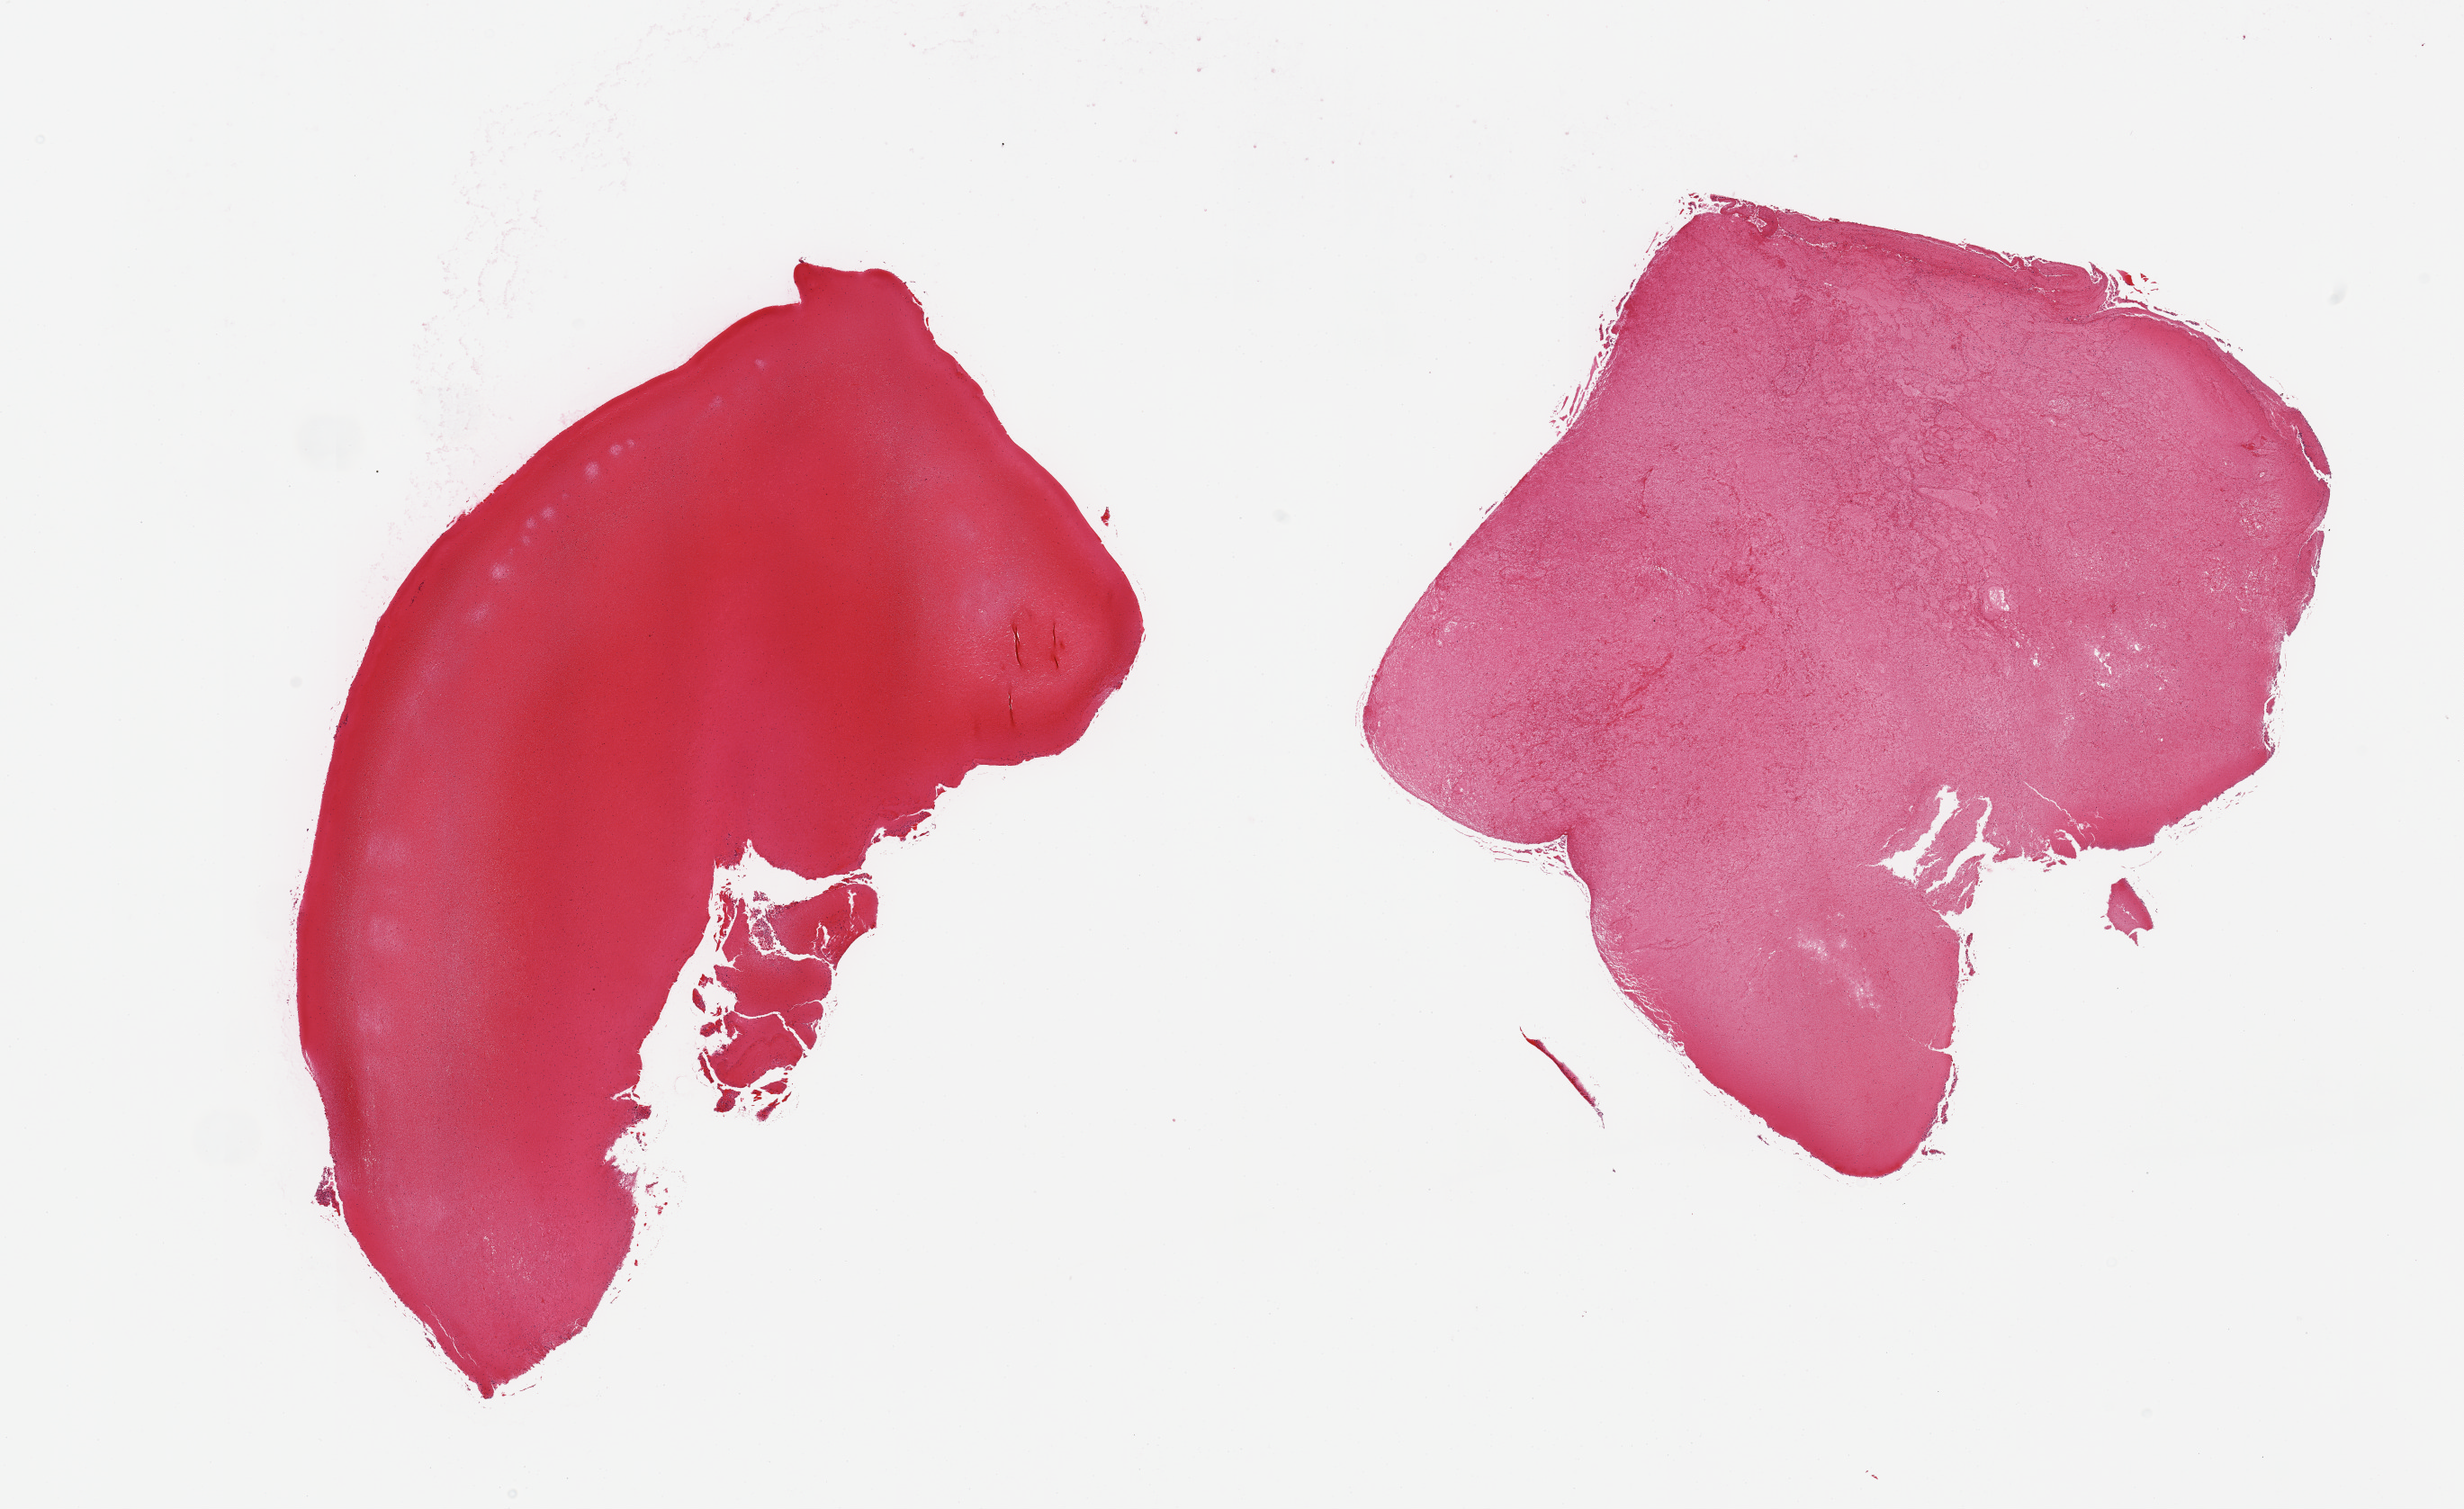
Hematoxylin and eosin (H&E) whole-slide image, low-resolution overview of the scanned area, about 21.7 x 13.3 mm (from a 20x scan), PAXgene-fixed, paraffin-embedded tissue, sampled site (target tissue): spleen, donor tissue sample. Donor sex: male.
Review note (as recorded): 2 pieces; blood clot.